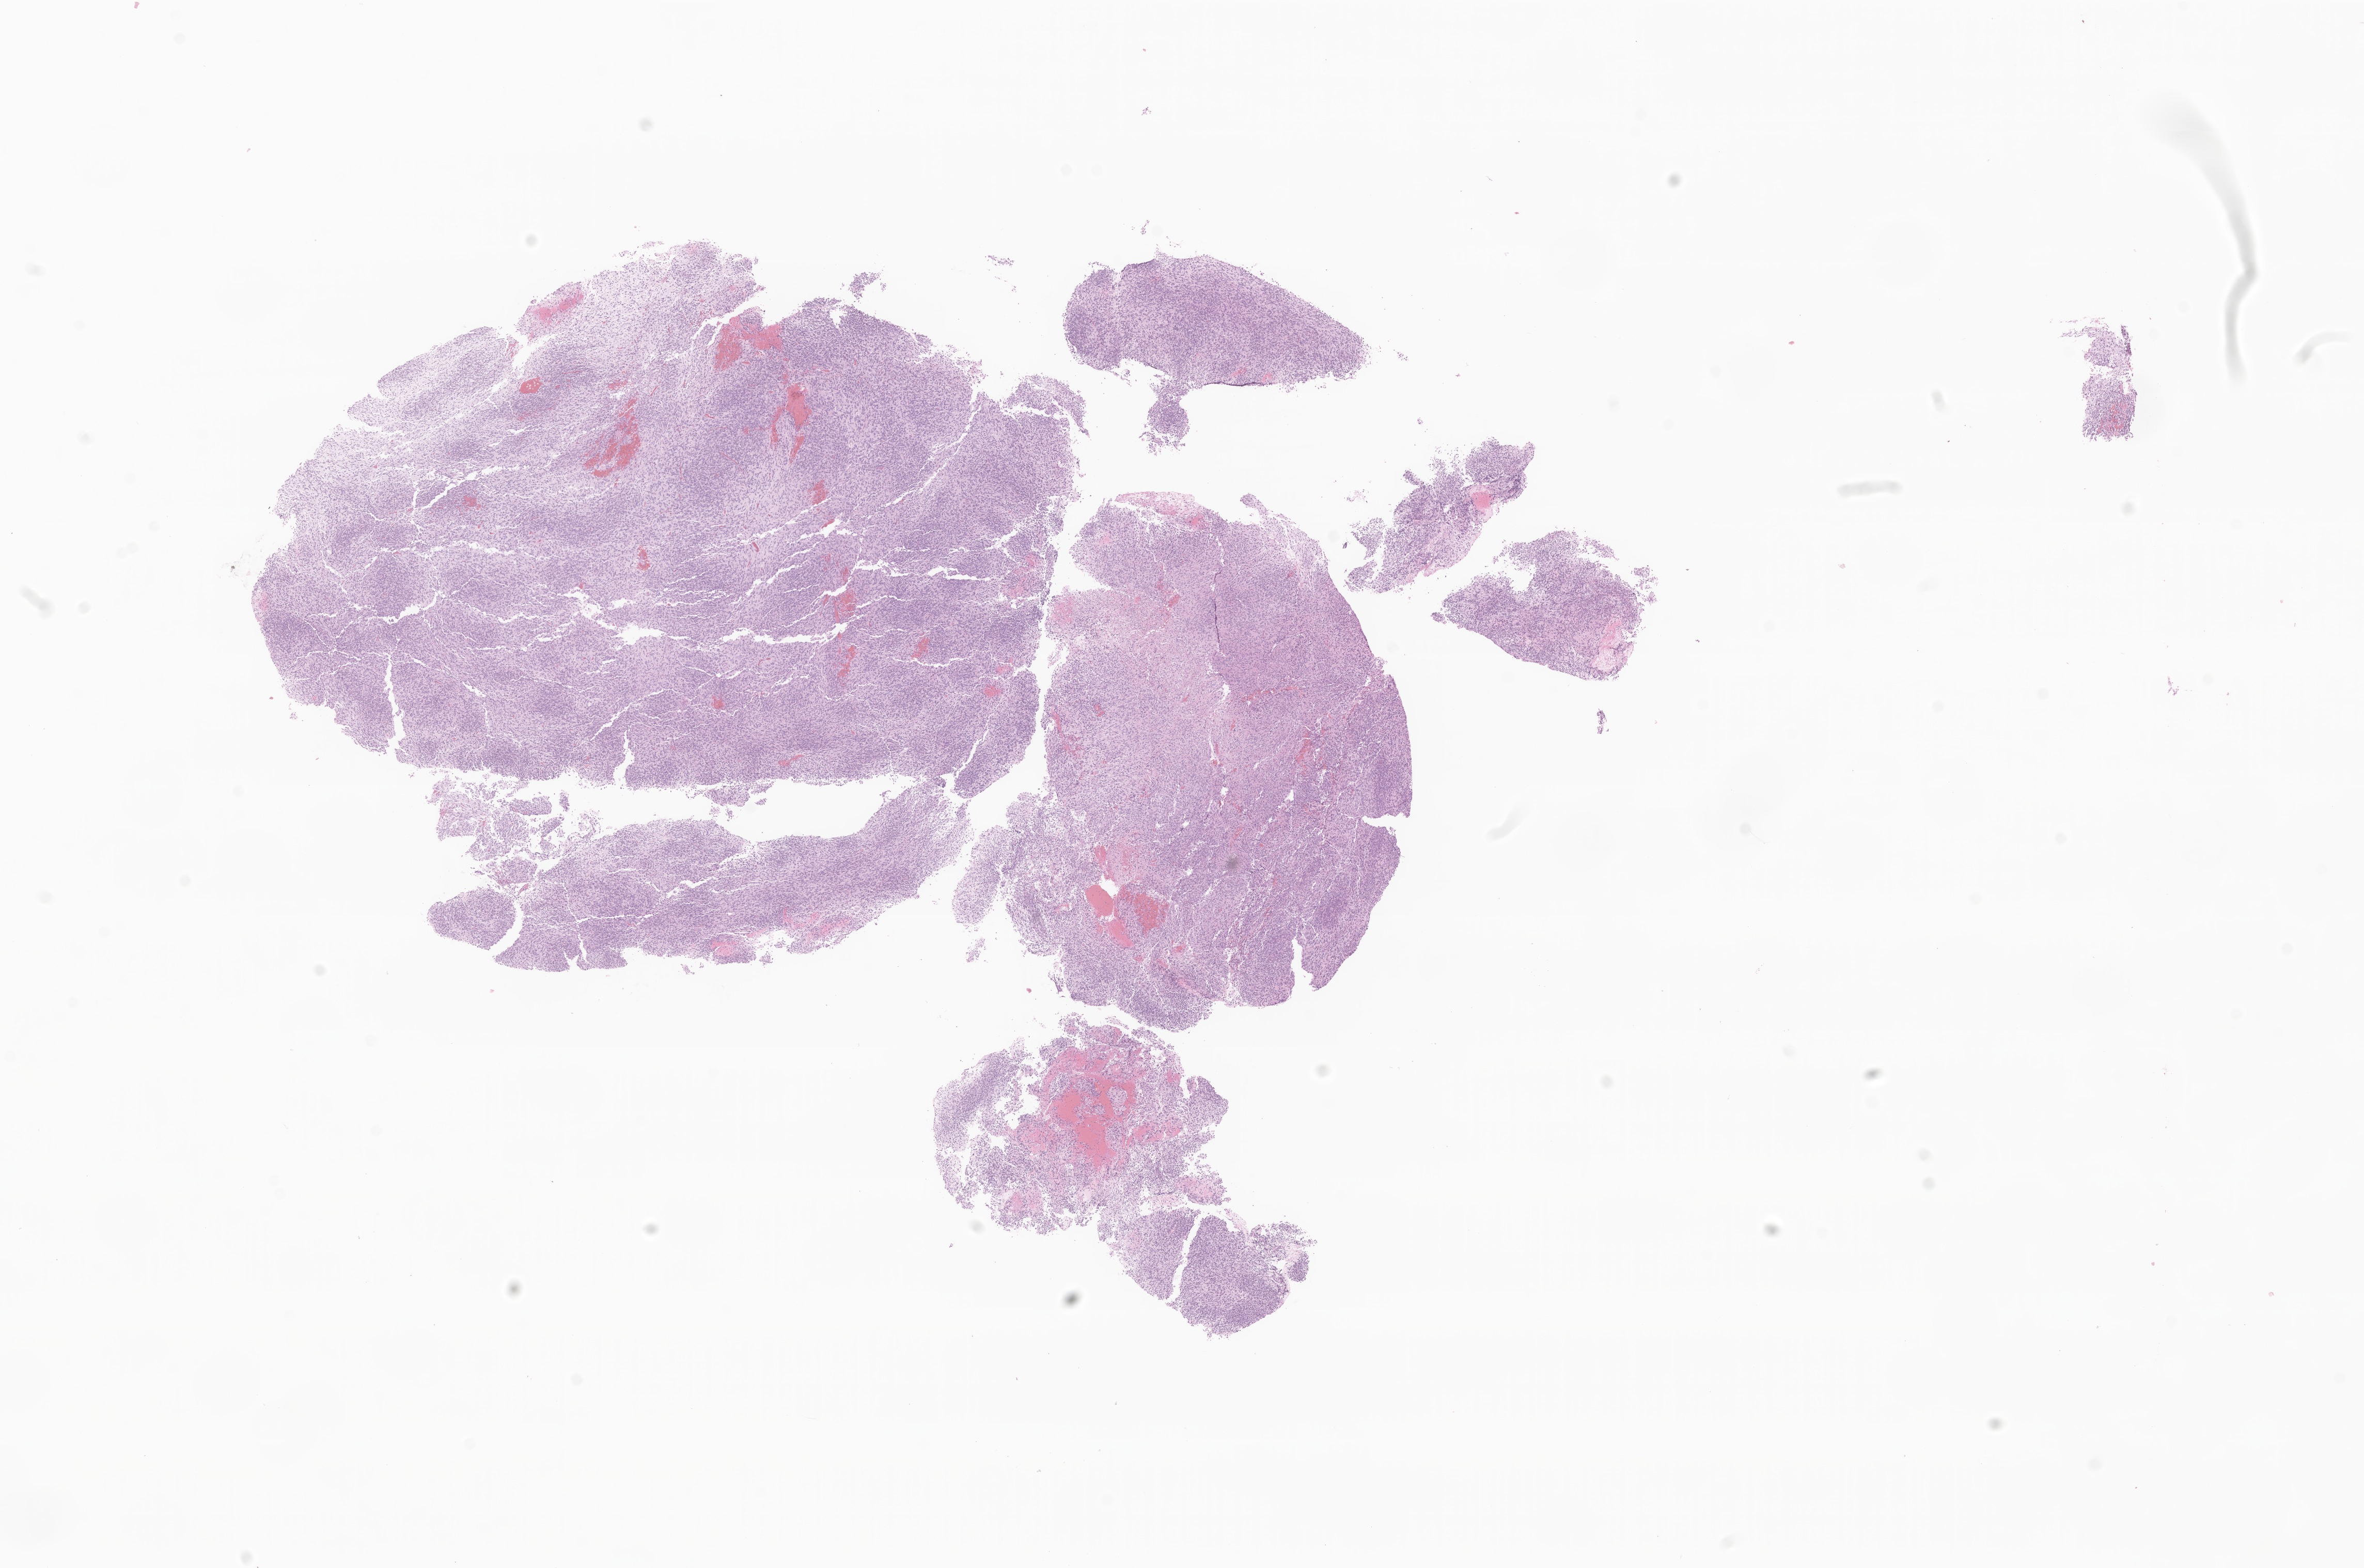
Whole-slide image, H&E stain of tumor tissue from the brain, a low-resolution overview of the entire scanned area, about 19.3 x 12.8 mm, FFPE section. Patient: male, age 166 months.
- diagnosis: Medulloblastoma, NOS